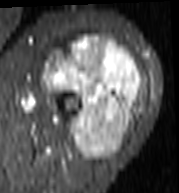
MRI of an extremity soft-tissue mass, one axial slice. Slice 60 of 103 in the series (ordered by position). STIR. MR volume resampled by the dataset authors to the PET/CT grid (not the native acquisition matrix). 179 × 193 image matrix. Female patient. From the clinical record (not read from this slice): histological type: undifferentiated – high grade; grade: high; site of the primary tumour: left thigh.
Outlined on this slice (expert contour drawn on MRI and transferred to this co-registered scan by the dataset authors):
- gross tumour volume including surrounding oedema: bounding box <43,37,142,161> (left, top, right, bottom; pixels)
- gross tumour volume (mass): <43,37,142,161>